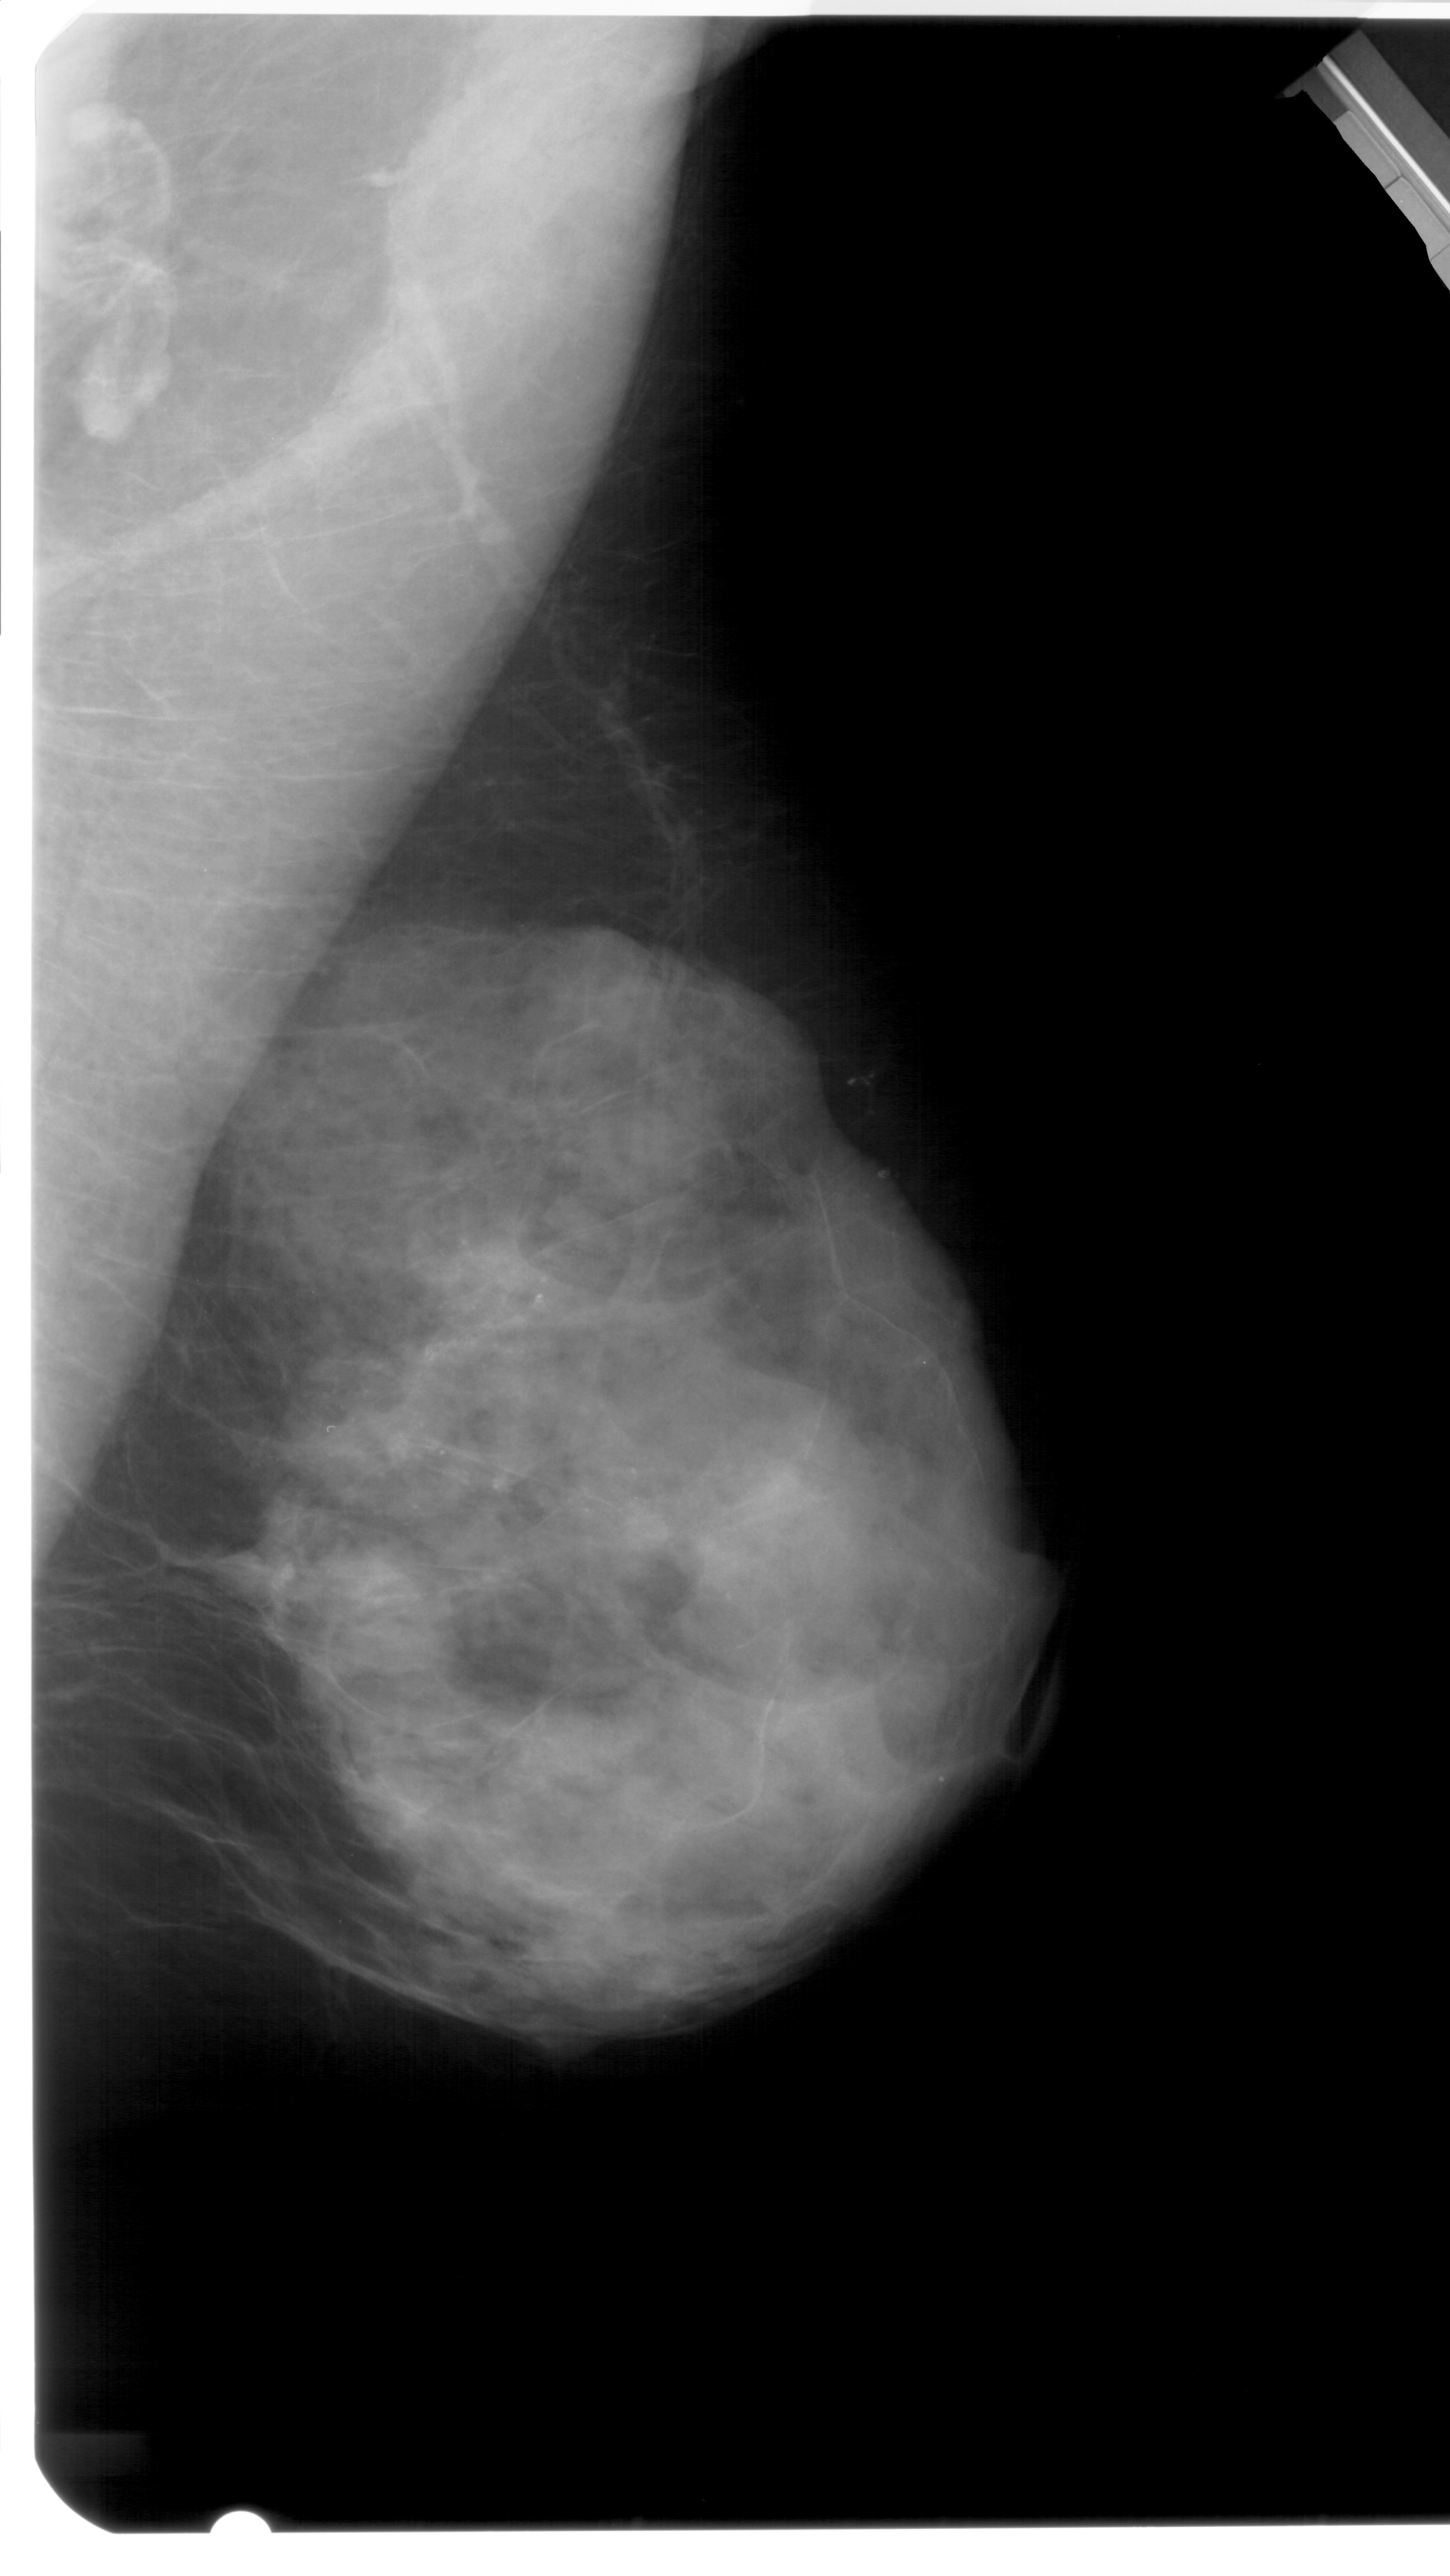
Digitized screen-film mammogram, right breast, mediolateral oblique (MLO) view, breast composition: extremely dense (BI-RADS density category 4 of 4).
Marked abnormality: calcifications, morphology pleomorphic, distribution segmental; BI-RADS assessment category 4; subtlety rating 3 on a 1 (subtle) to 5 (obvious) scale; pathology (as recorded): benign.